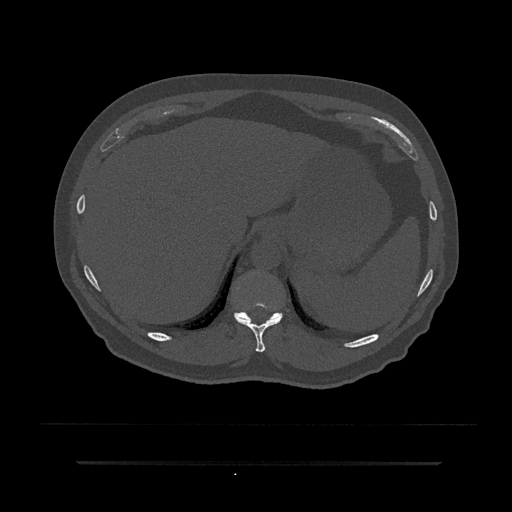
CT including the spine, one axial slice; slice 304 of 797 in the series (ordered by position); bone window (W 1800 / L 400 HU); 0.5 mm slice thickness; 512 × 512 image matrix, field of view 464 × 464 mm. Patient: male, 59 years. From the clinical record (not read from this slice): primary cancer: bile ducts; vertebrae with lytic lesions (as recorded): T10.
Outlined on this slice (semi-automatic segmentation, software-assisted and operator-edited):
- T10 vertebra: bounding box <235,301,282,353> (left, top, right, bottom; pixels)
- T11 vertebra: <234,312,282,322>